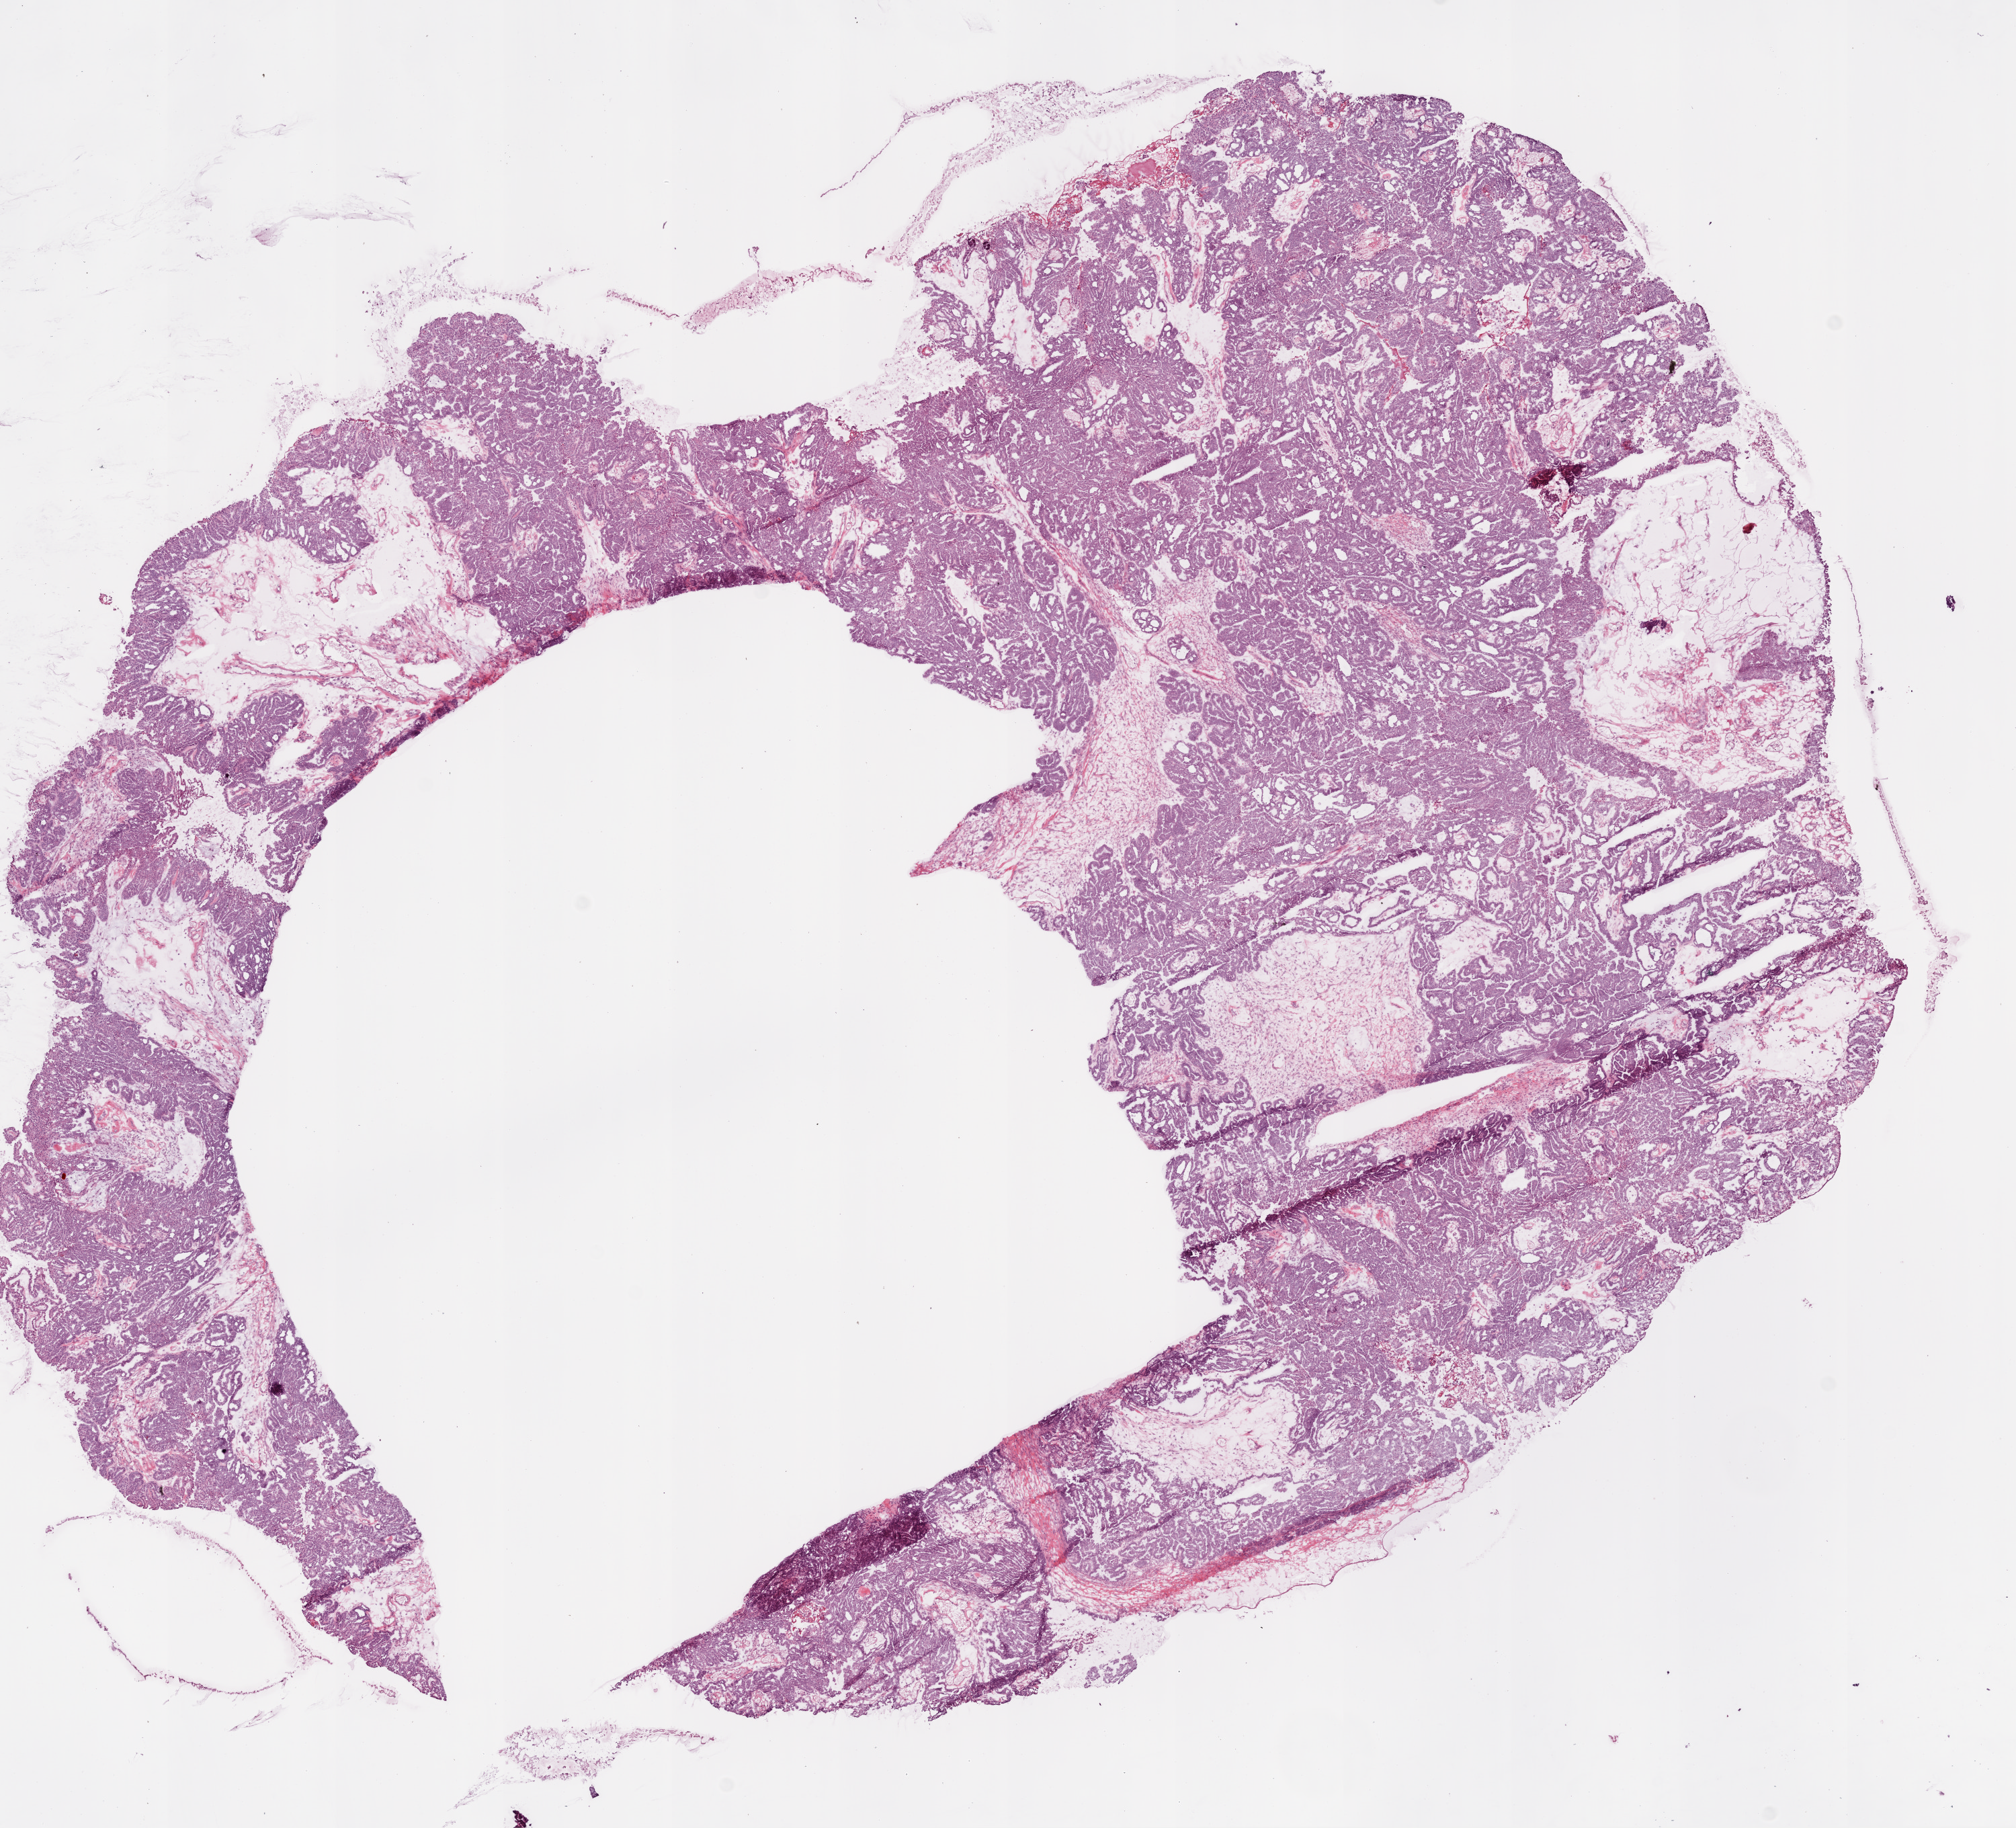
H&E whole-slide image — shown as a low-resolution overview of the whole scanned area (about 12.0 x 10.9 mm), frozen section from the bottom of the tissue portion, sample: primary tumour, ovary. Female patient; age at initial diagnosis 64 years. Histologic grade: G1 (well differentiated). Pathologist review of this section (percent, as recorded): tumour cells 94%, tumour nuclei 95%, normal cells 0%, stromal cells 5%, necrosis 1%.
• FIGO stage: IIIC
• laterality: bilateral
• histologic diagnosis: Serous cystadenocarcinoma, NOS